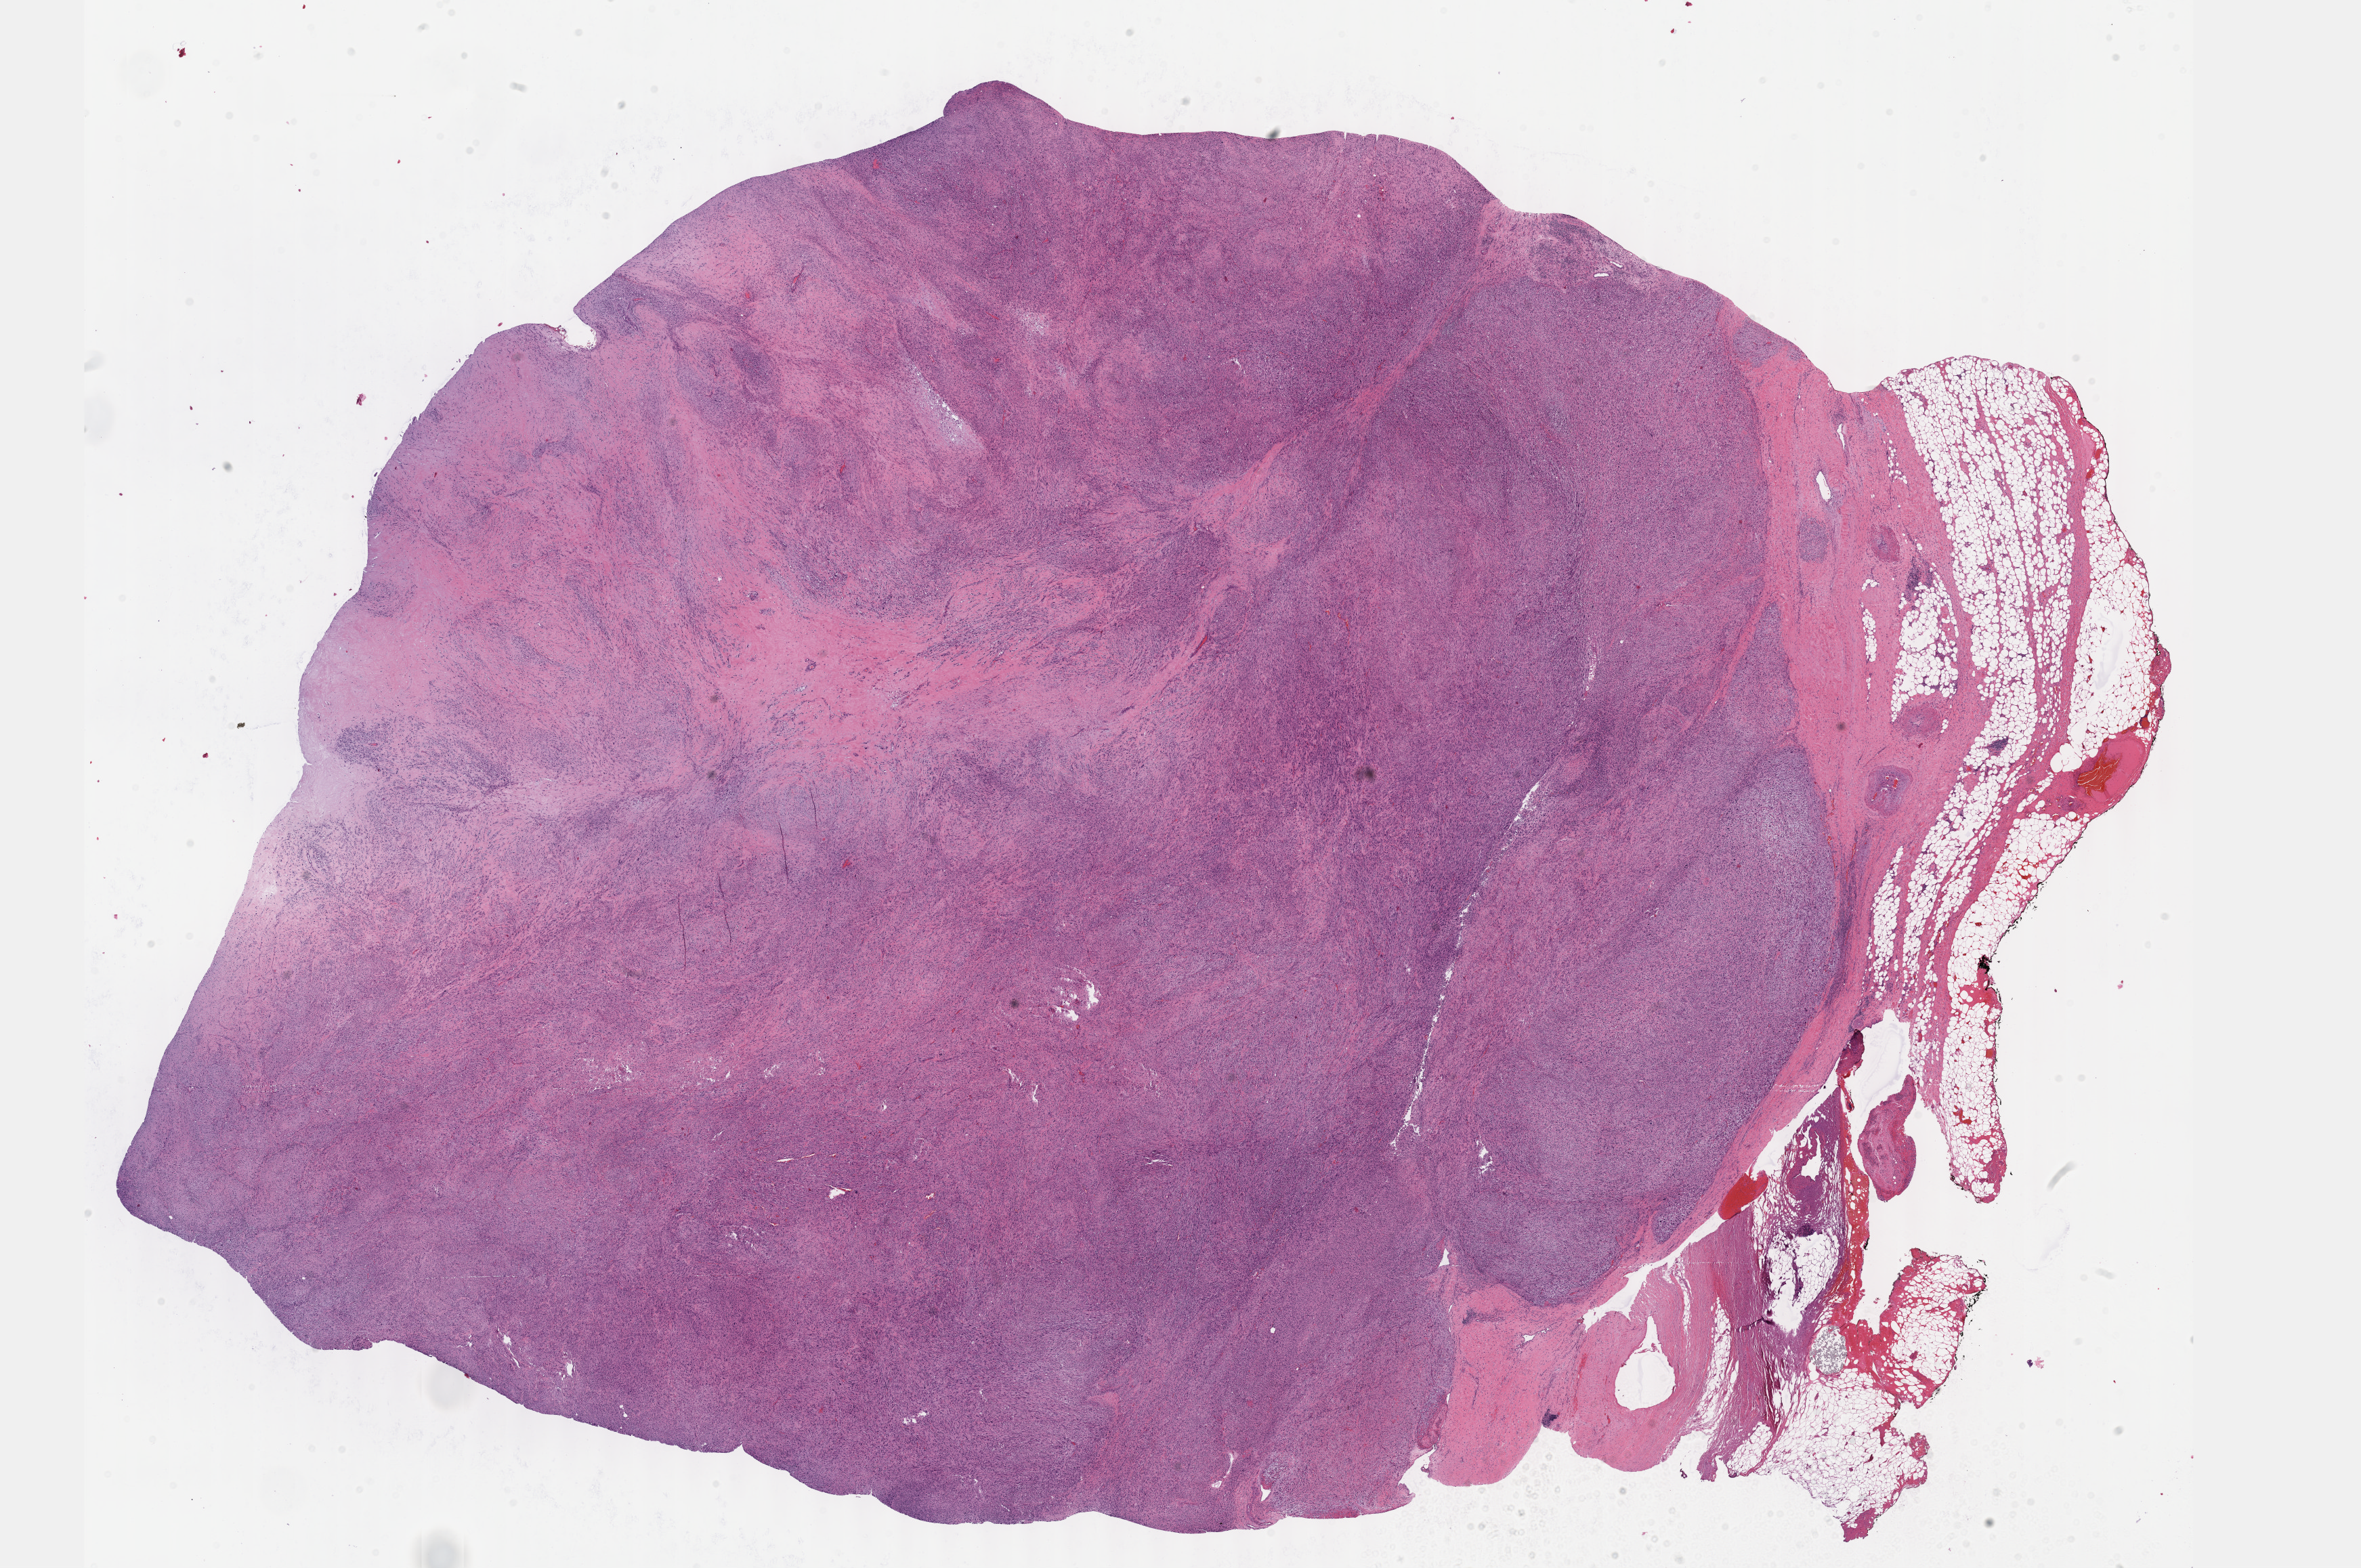
H&E whole-slide image, whole scanned area (about 28.2 x 18.7 mm, from a 40x scan) shown as a low-resolution overview; formalin-fixed paraffin-embedded (FFPE) diagnostic section; connective, subcutaneous and other soft tissues, primary tumour sample. Male, age 66 years at initial diagnosis.
* histologic diagnosis: Undifferentiated sarcoma